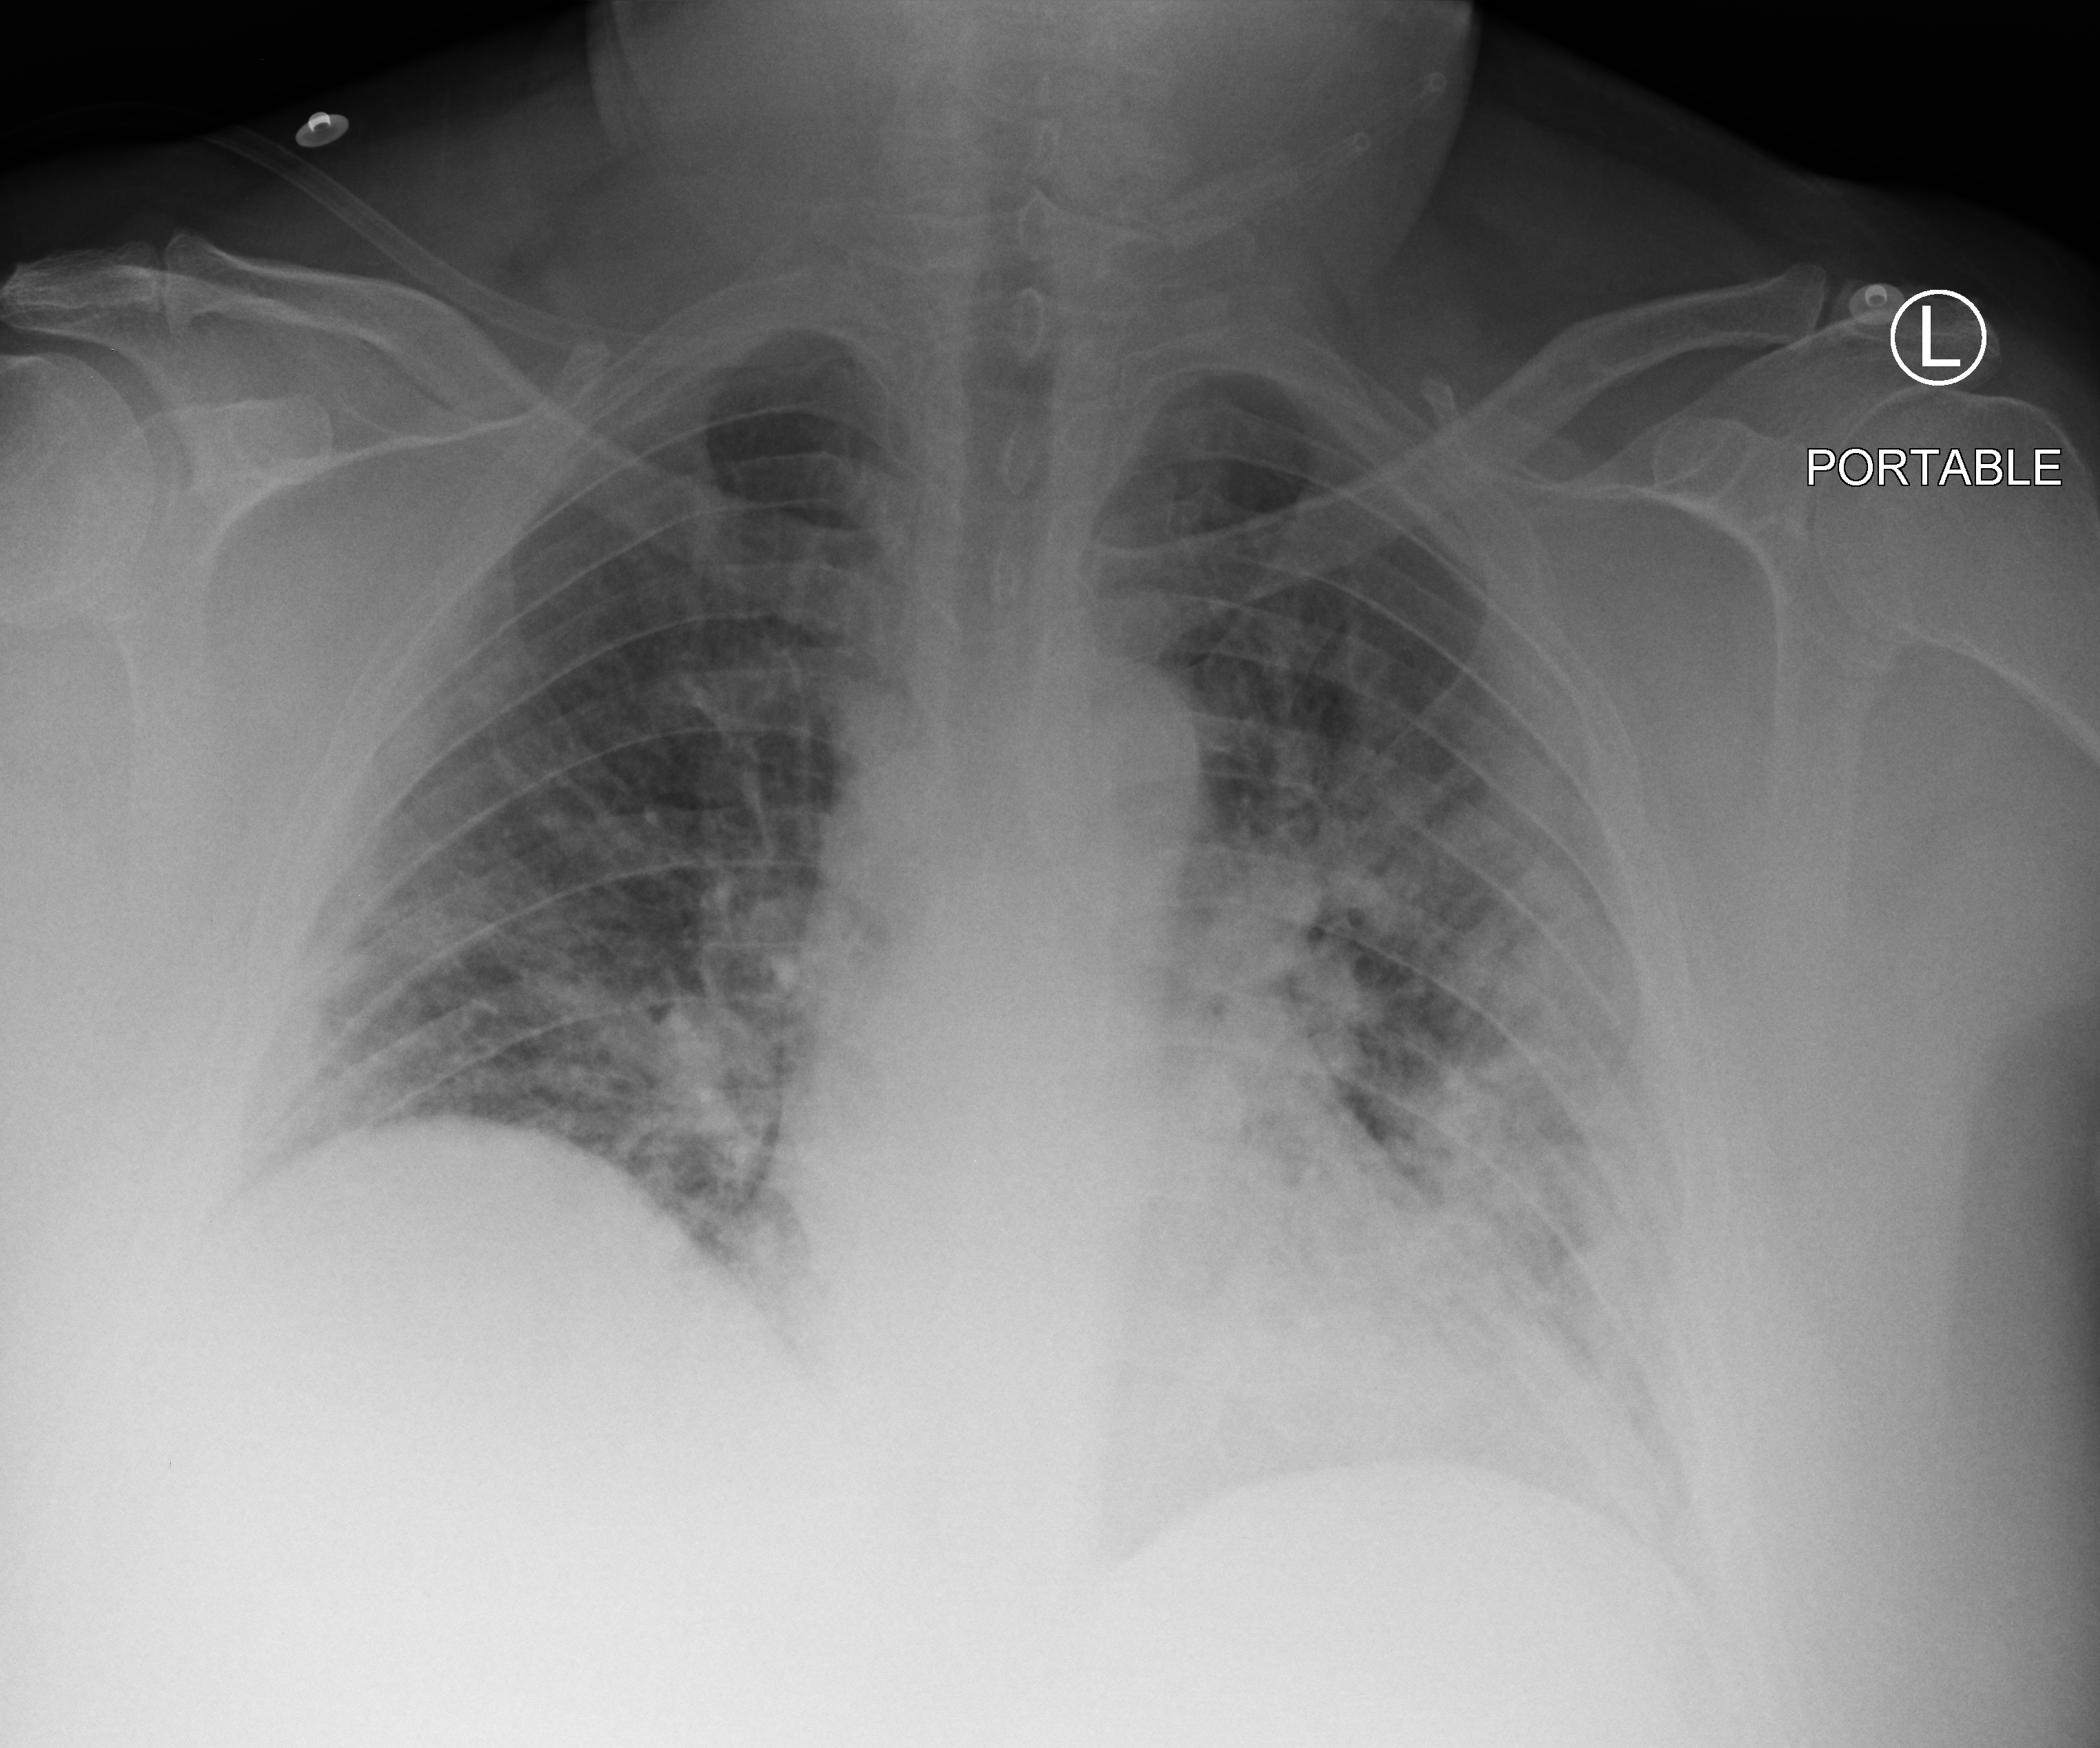
Portable chest radiograph, anteroposterior (AP) projection. Male patient hospitalised with COVID-19, age 18–59 years.
Admission-level facts for this patient (not findings on this image; timing relative to this image not recorded): admitted to intensive care during this hospital stay: no; length of hospital stay: 12 days.